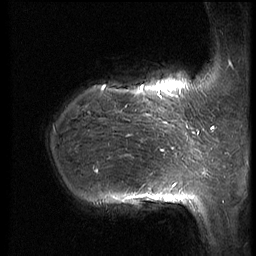
Breast MRI (dynamic contrast-enhanced), one sagittal slice. Slice 18 of 66 in the series (ordered by position). Dynamic contrast-enhanced series, image 2 of 3 at this slice position (ordered by acquisition). 1.5 T. TE 4.2 ms, TR 8.9 ms. 2.5 mm slice thickness. 256 × 256 image matrix. Female patient, age 39 years. From the clinical record (not read from this slice): setting: breast cancer imaged before/during neoadjuvant chemotherapy; receptor status: HER2-positive.
Outlined on this slice (semi-automatic segmentation, software-assisted and operator-edited):
- analysis volume of interest (the breast-tissue region the enhancement analysis was run in; not a lesion): bounding box <40,75,188,218> (left, top, right, bottom; pixels)
- tumour enhancement mask (voxels above the 140 % enhancement threshold inside the analysis volume of interest): <102,86,175,202>